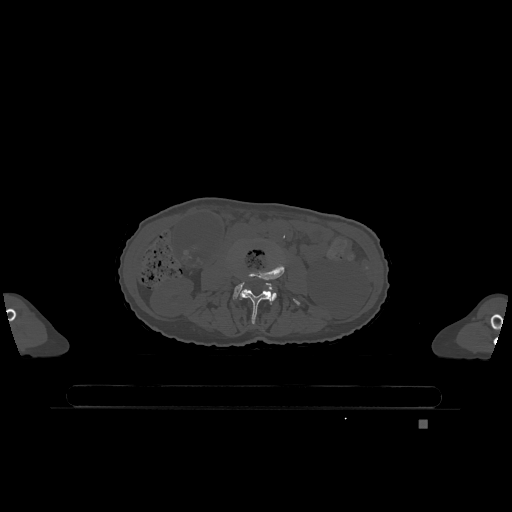
CT including the spine, one axial slice. Slice 342 of 1317 in the series (ordered by position). Bone window (W 1800 / L 400 HU). 0.5 mm slice thickness. 512 × 512 image matrix, field of view 500 × 500 mm. Female patient, age 74 years. From the clinical record (not read from this slice): primary cancer: lung.
Outlined on this slice (semi-automatically segmented with operator editing):
- L3 vertebra: bounding box [x1, y1, x2, y2] px = [238, 260, 300, 324]
- L4 vertebra: [233, 282, 277, 301]